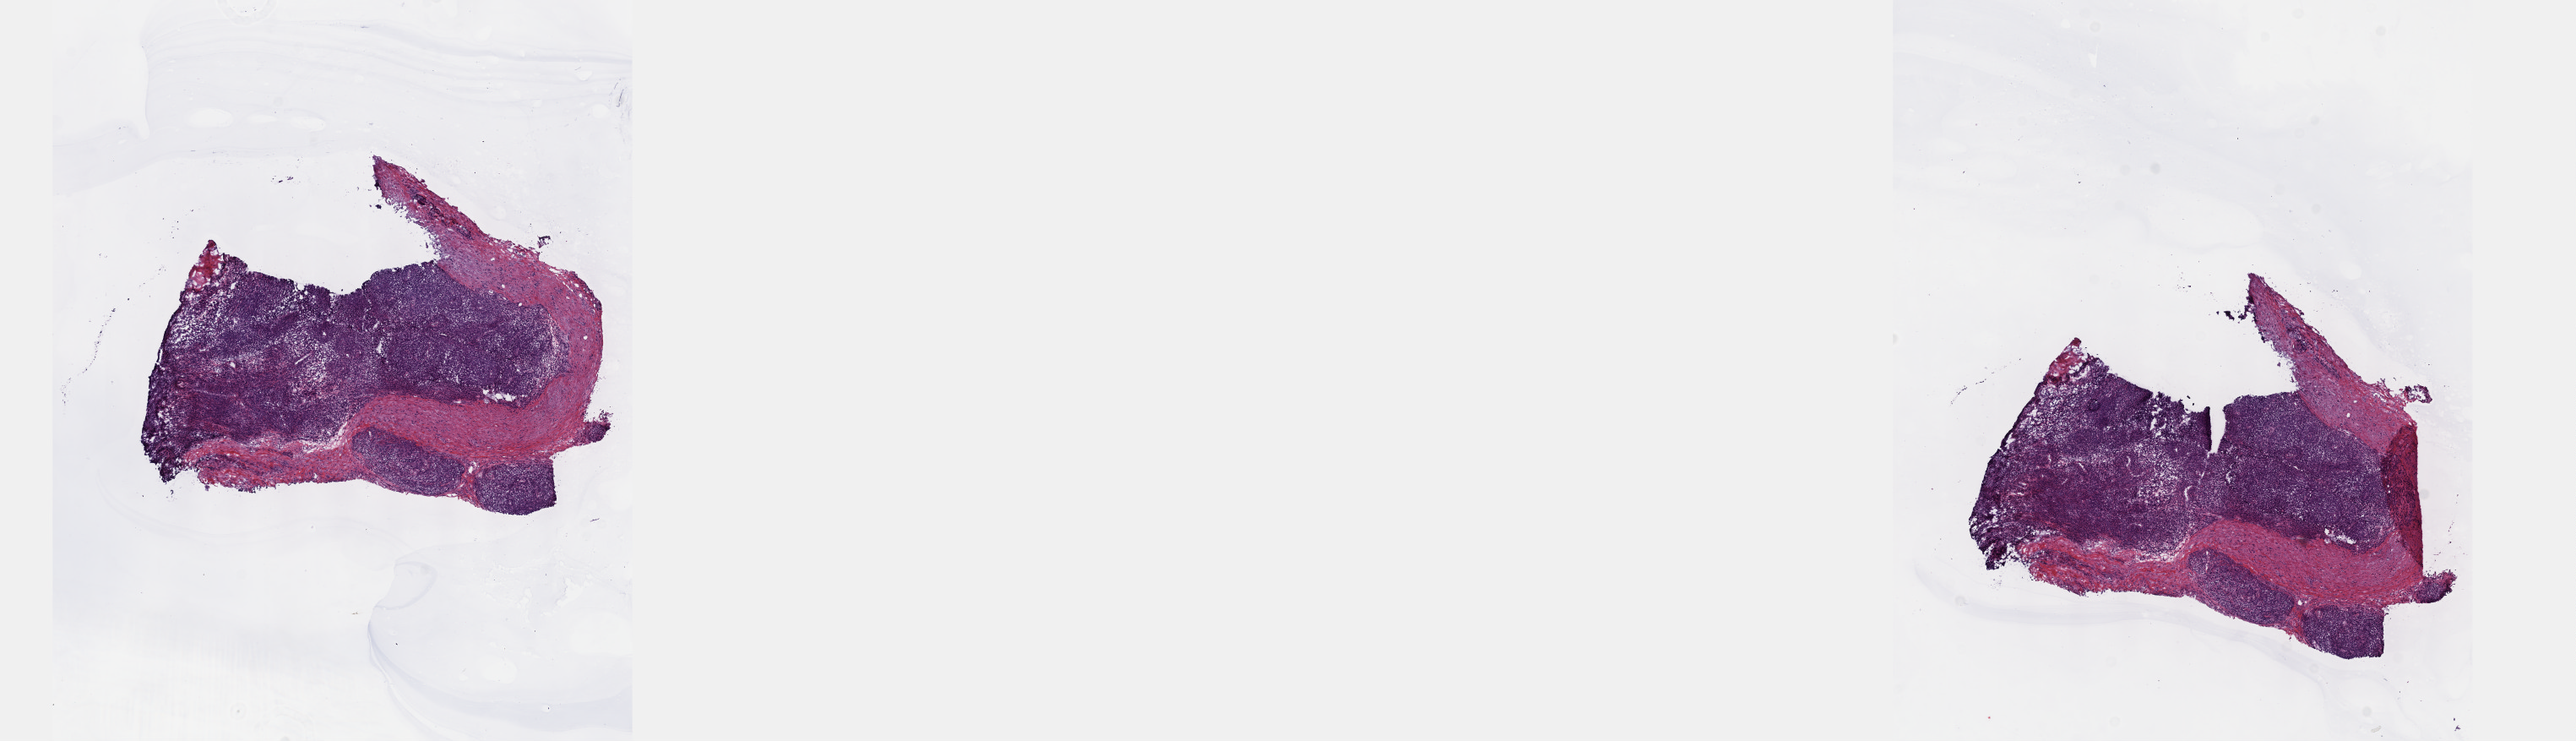
Whole-slide histology image, Hematoxylin and eosin (H&E) stained, shown as a low-resolution overview of the whole scanned area (about 24.6 x 7.1 mm, from a 40x scan). Frozen section from the top of the tissue portion. Metastatic tumour sample, sampled site: connective, subcutaneous and other soft tissues of thorax. Patient: male, age at initial diagnosis 70 years. Slide review estimates, as recorded: tumour cells 80%, tumour nuclei 80%, normal cells 0%, stromal cells 20%, necrosis 0%. Infiltration values recorded for this section: lymphocyte infiltration 2%, monocyte infiltration 1%, neutrophil infiltration 1%.
This section: metastatic tumour tissue. Patient diagnosis: Malignant melanoma, NOS.